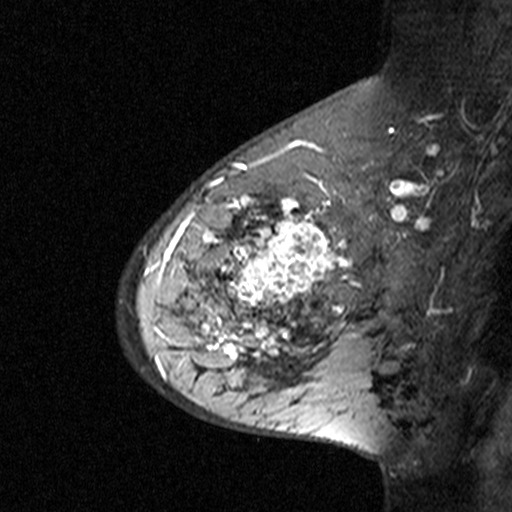
Breast MRI (dynamic contrast-enhanced), one sagittal slice. Slice 27 of 44 in the series (ordered by position). Dynamic contrast-enhanced study with each time point stored as its own series, time point 3 of 4 at this slice position (ordered by acquisition time). 1.5 T. TE 4.5 ms, TR 11 ms. 3 mm slice thickness. 512 × 512 image matrix, field of view 200 × 200 mm. Patient: female, 65 years. From the clinical record (not read from this slice): setting: breast cancer imaged before/during neoadjuvant chemotherapy; receptor status: HER2-positive.
Structures marked on this image (semi-automatically segmented with operator editing):
- analysis volume of interest (the breast-tissue region the enhancement analysis was run in; not a lesion): bounding box (x1, y1, x2, y2) in pixels: (182, 190, 353, 361)
- tumour enhancement mask (voxels above the 90 % enhancement threshold inside the analysis volume of interest): (182, 195, 353, 359)